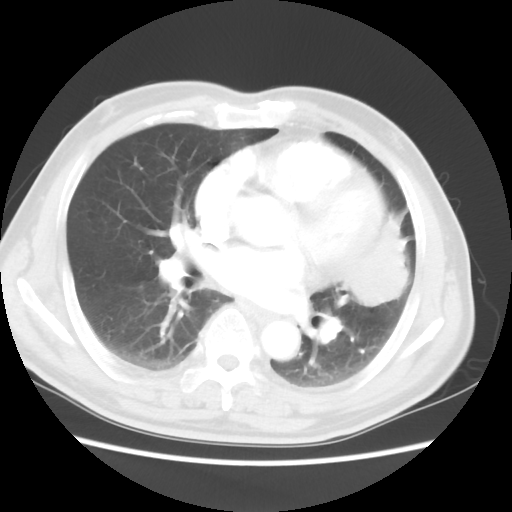
Chest CT, one axial slice. Slice 23 of 50 in the series (ordered by position). Lung window (W 1500 / L -600 HU). 5 mm slice thickness. 512 × 512 image matrix. Male patient, age 69 years. From the clinical record (not read from this slice): clinical TNM (as recorded): T3 N1 M1a.
Outlined on this slice (rectangle marked by the reading radiologist):
- lung tumour (recorded histology: squamous cell carcinoma): bounding box (x1, y1, x2, y2) in pixels: (330, 209, 415, 309)